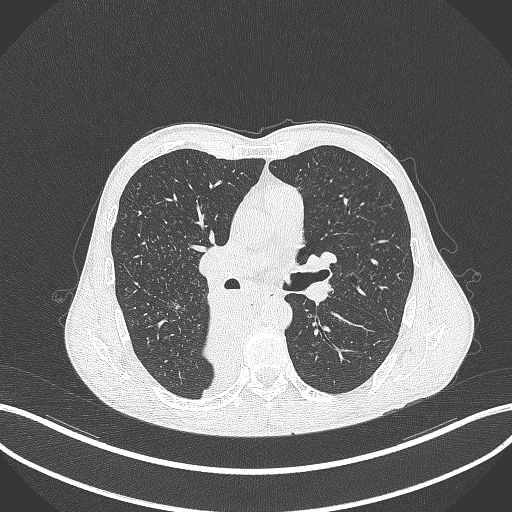
Chest CT, one axial slice; position 217 of 371 along the scan axis; reconstruction kernel B70f; 120 kVp; lung window (W 1500 / L -600 HU); 1 mm slice thickness; 512 × 512 image matrix, field of view 400 × 400 mm. Patient: male, 58 years. From the clinical record (not read from this slice): clinical TNM (as recorded): T3 N1 M1.
Annotated regions visible in this slice (bounding box drawn by a radiologist):
- lung tumour (recorded histology: squamous cell carcinoma): bounding box <194,289,244,375> (left, top, right, bottom; pixels)